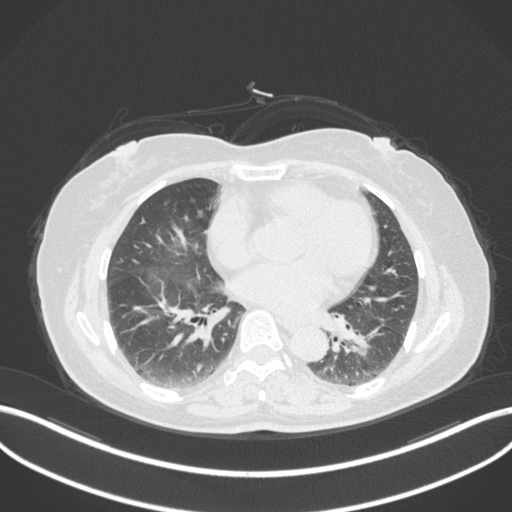
Chest CT, one axial slice; slice 164 of 307 in the series (ordered by position); reconstruction kernel B31f; 120 kVp; lung window (W 1500 / L -600 HU); 1 mm slice thickness; 512 × 512 image matrix, field of view 400 × 400 mm. Female patient, age 59 years. From the clinical record (not read from this slice): clinical TNM (as recorded): T2a N0 M0; histopathological grade: G2-3.
Structures marked on this image (bounding box drawn by a radiologist):
- lung tumour (recorded histology: adenocarcinoma): bounding box <348,322,387,361> (left, top, right, bottom; pixels)